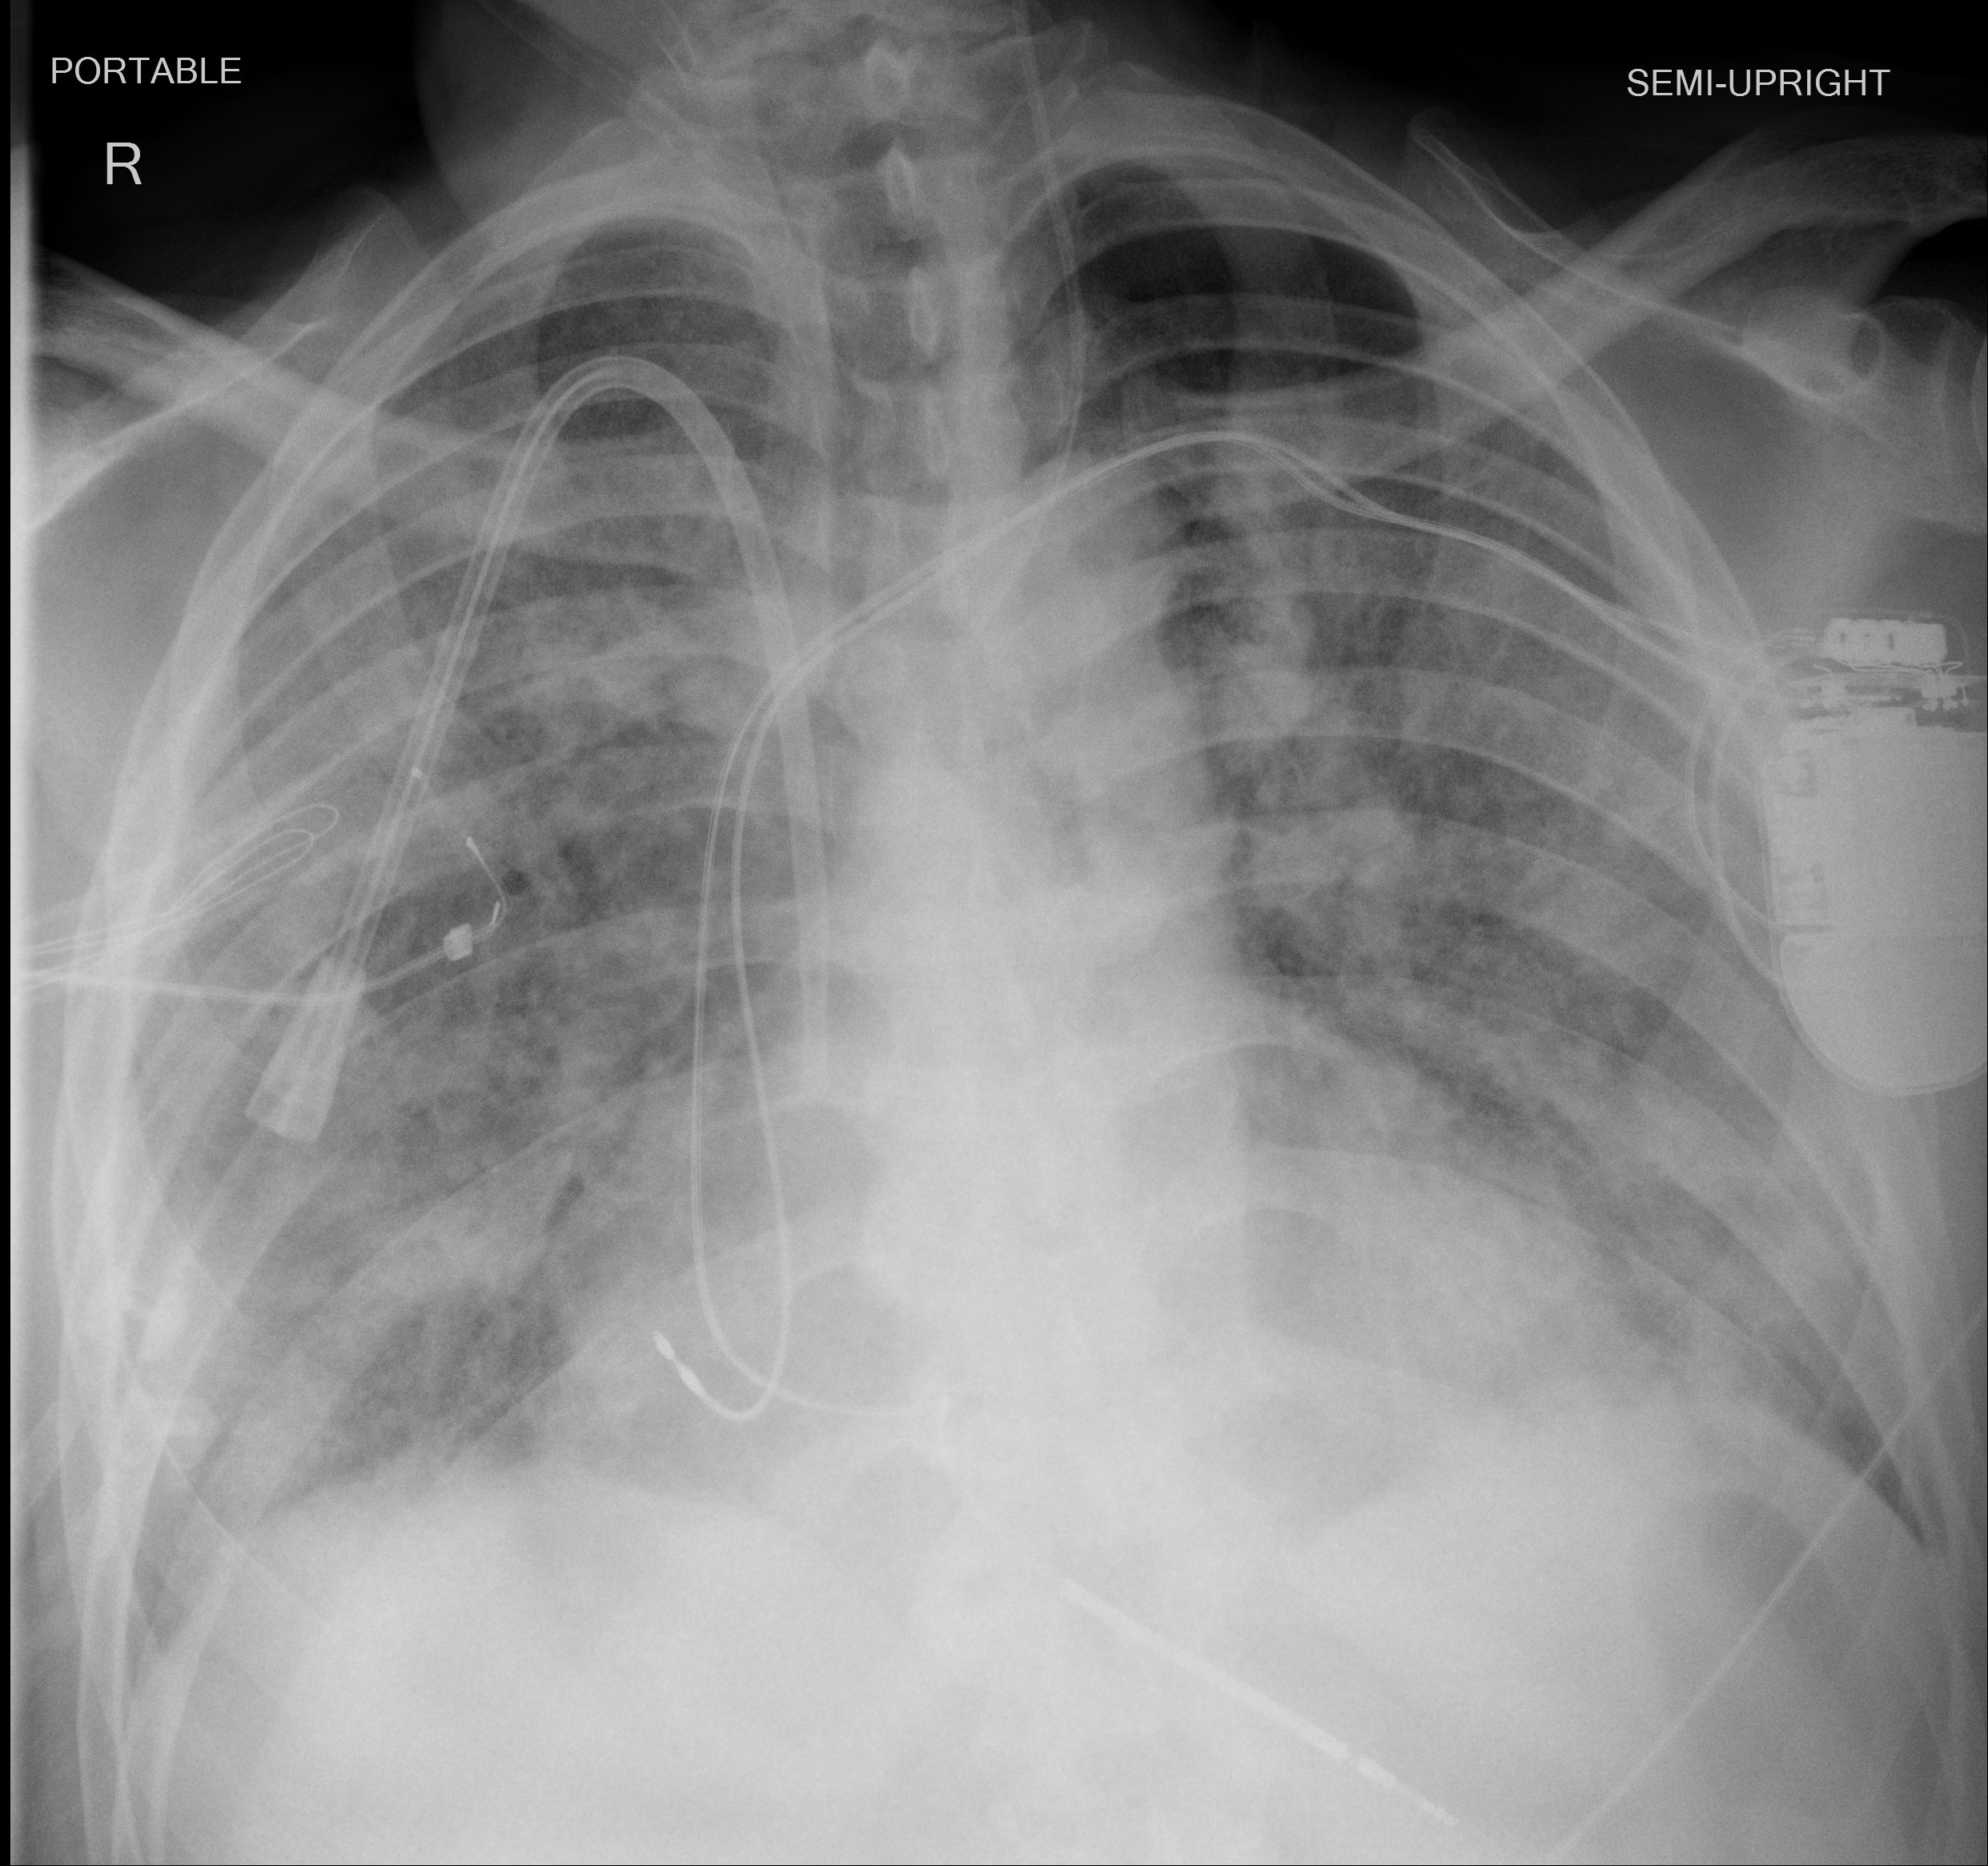
Portable chest radiograph, AP projection. Male patient, age 60 years; imaged 11 days after the COVID-19 diagnosis.
Radiologist key findings (as recorded): worsening consolidative changes in both mid and lower lung zones. Minimal bilateral pleural effusions.